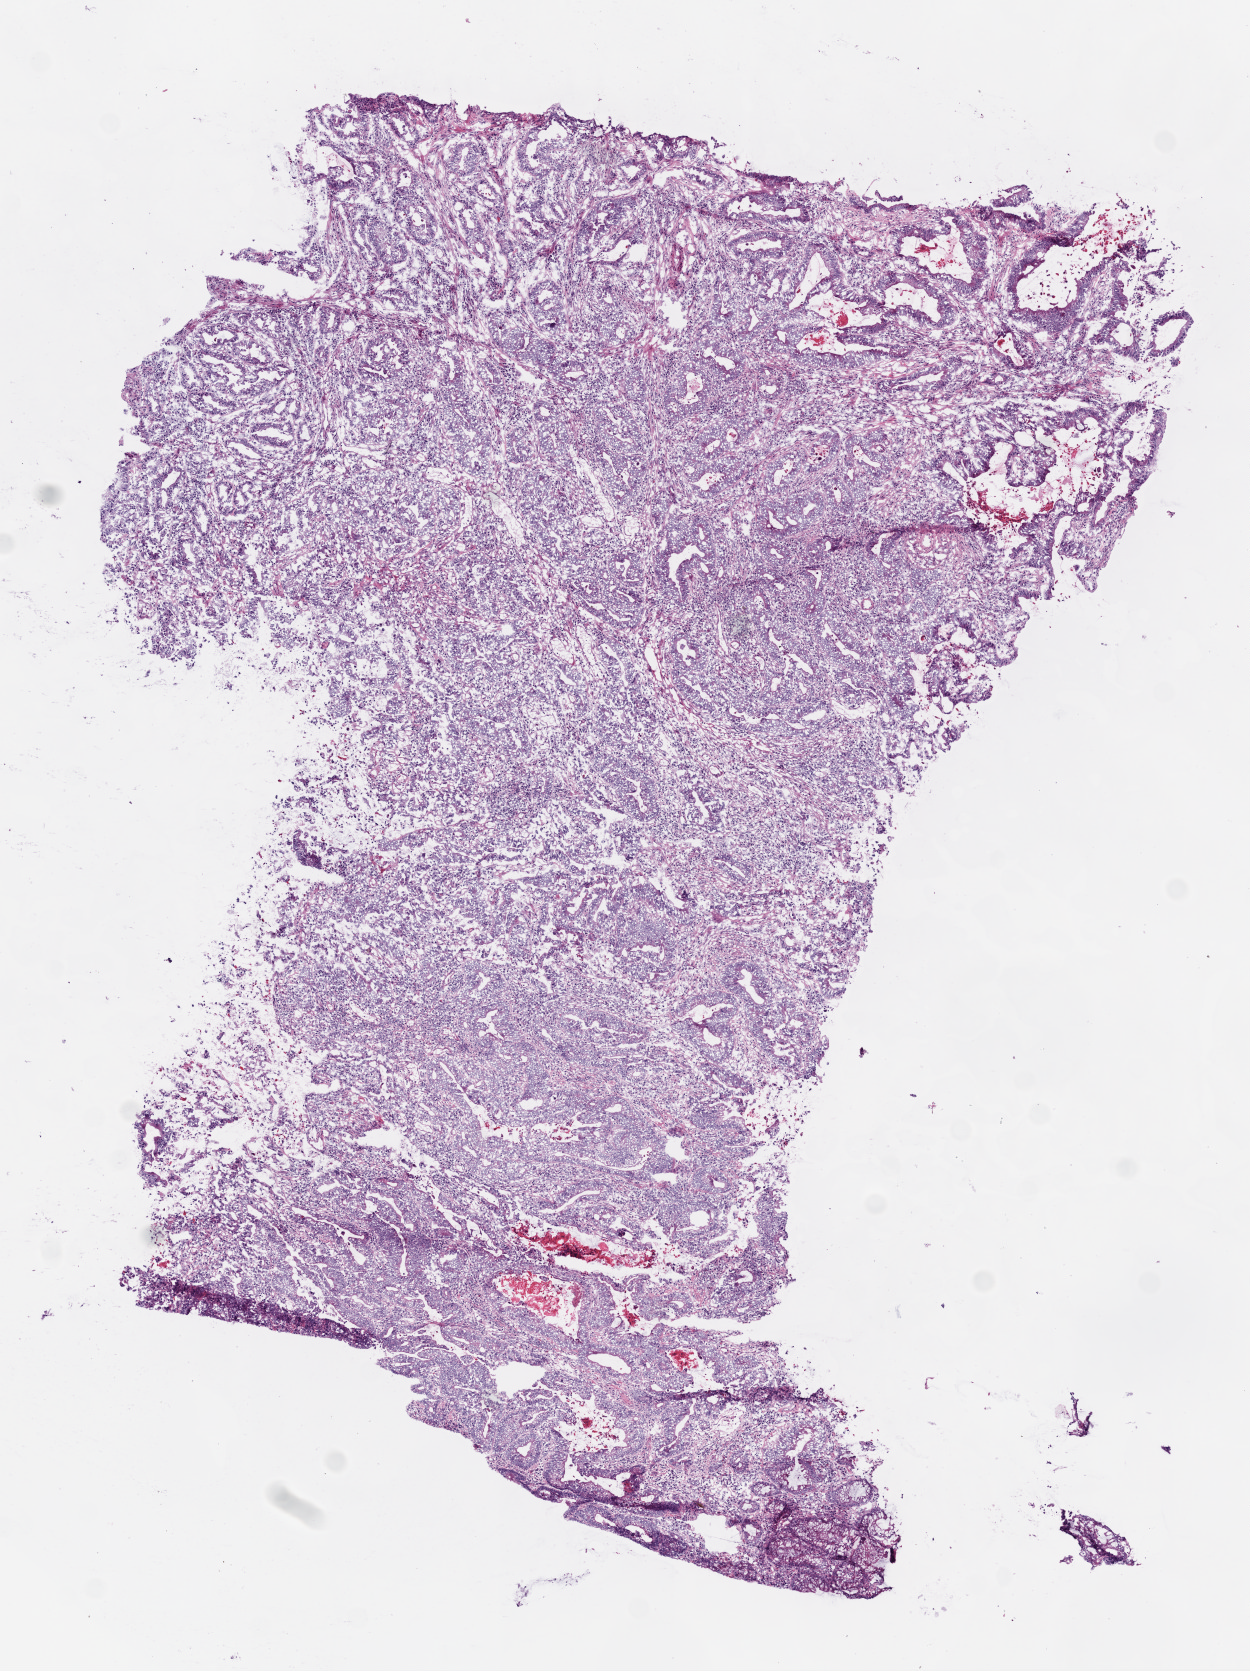
Hematoxylin and eosin (H&E) stained whole-slide image — a low-resolution overview of the entire scanned area, about 5.0 x 6.7 mm (from a 20x scan); frozen section from the bottom of the tissue portion; sample: primary tumour, colon. Female, age 73 years at initial diagnosis. Composition of this section per pathologist review: tumour cells 70%, tumour nuclei 70%, normal cells 10%, stromal cells 15%, necrosis 5%.
Lymph nodes positive (case pathology): 0 of 16 examined. TNM: T3 N0. Diagnosis: Adenocarcinoma, NOS (ascending colon). AJCC pathologic stage: IIB (6th edition).